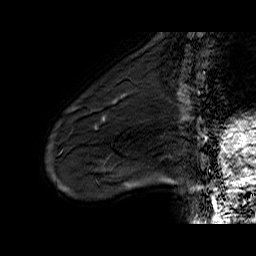
Breast MRI (dynamic contrast-enhanced), one sagittal slice; slice 14 of 60 in the series (ordered by position); dynamic contrast-enhanced series, time point 2 of 6 at this slice position (early post-contrast); 1.5 T; TE 6.5 ms, TR 32.9 ms; 256 × 256 image matrix, field of view 200 × 200 mm. Female patient. From the clinical record (not read from this slice): setting: breast cancer imaged before/during neoadjuvant chemotherapy; receptor status: HER2-positive.
Annotated regions visible in this slice (semi-automatic segmentation, software-assisted and operator-edited):
- analysis volume of interest (the breast-tissue region the enhancement analysis was run in; not a lesion): bounding box (x1, y1, x2, y2) in pixels: (72, 88, 133, 137)
- tumour enhancement mask (voxels above the 100 % enhancement threshold inside the analysis volume of interest): (72, 101, 117, 129)